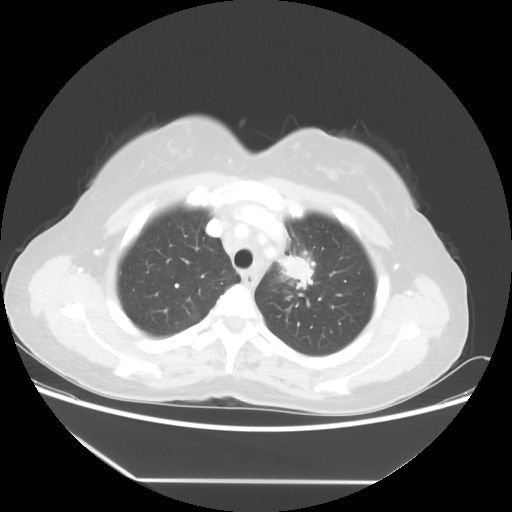
Chest CT, one axial slice; position 42 of 52 along the scan axis; 100 kVp; lung window (W 1500 / L -600 HU); 512 × 512 image matrix, field of view 390 × 390 mm. Female patient, age 50 years. Case-level facts recorded for this patient, not image findings: clinical TNM (as recorded): T2 N3 M0.
Outlined on this slice (rectangle marked by the reading radiologist):
- lung tumour (recorded histology: adenocarcinoma): bounding box <271,241,318,304> (left, top, right, bottom; pixels)